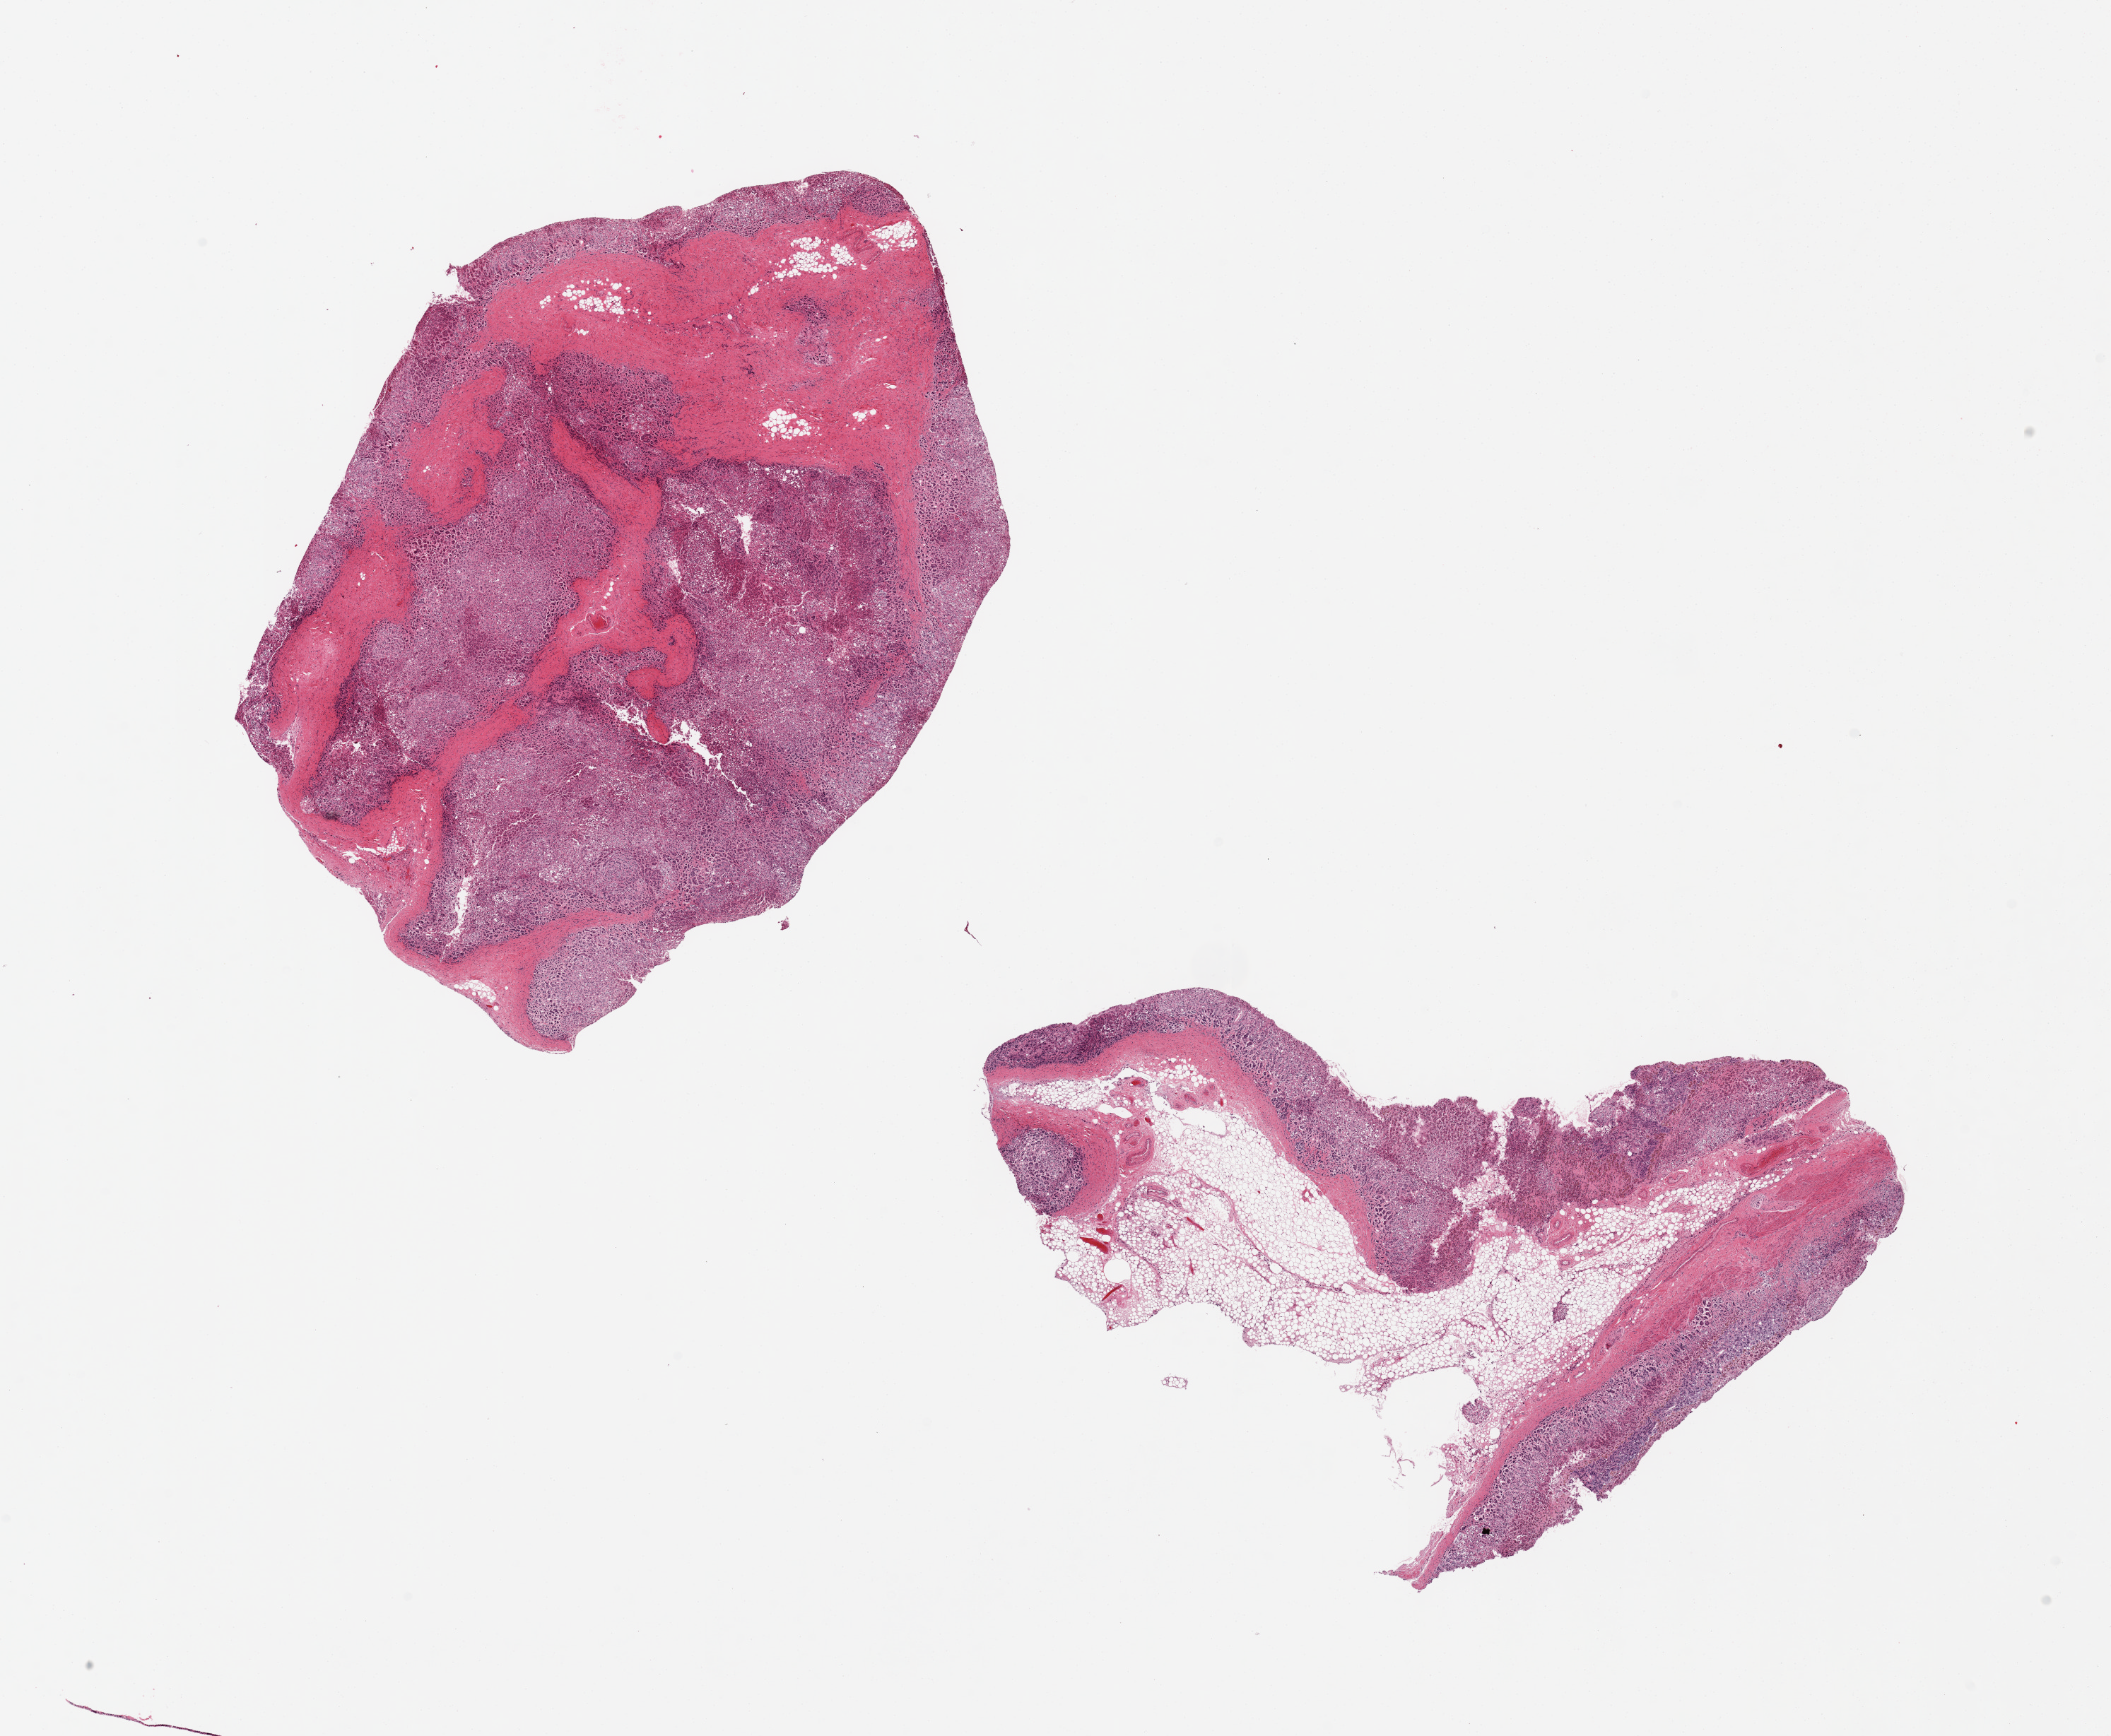
Digitized haematoxylin and eosin-stained section, a low-resolution overview of the entire scanned area, about 23.6 x 19.4 mm (slide scanned at 20x). PAXgene-fixed paraffin-embedded (PFPE) section. Section of adrenal gland (target tissue). Donor tissue sample. Donor: male.
Pathologist's review note for this sample: 2 pieces, both ~50% fibroadipose tissue.